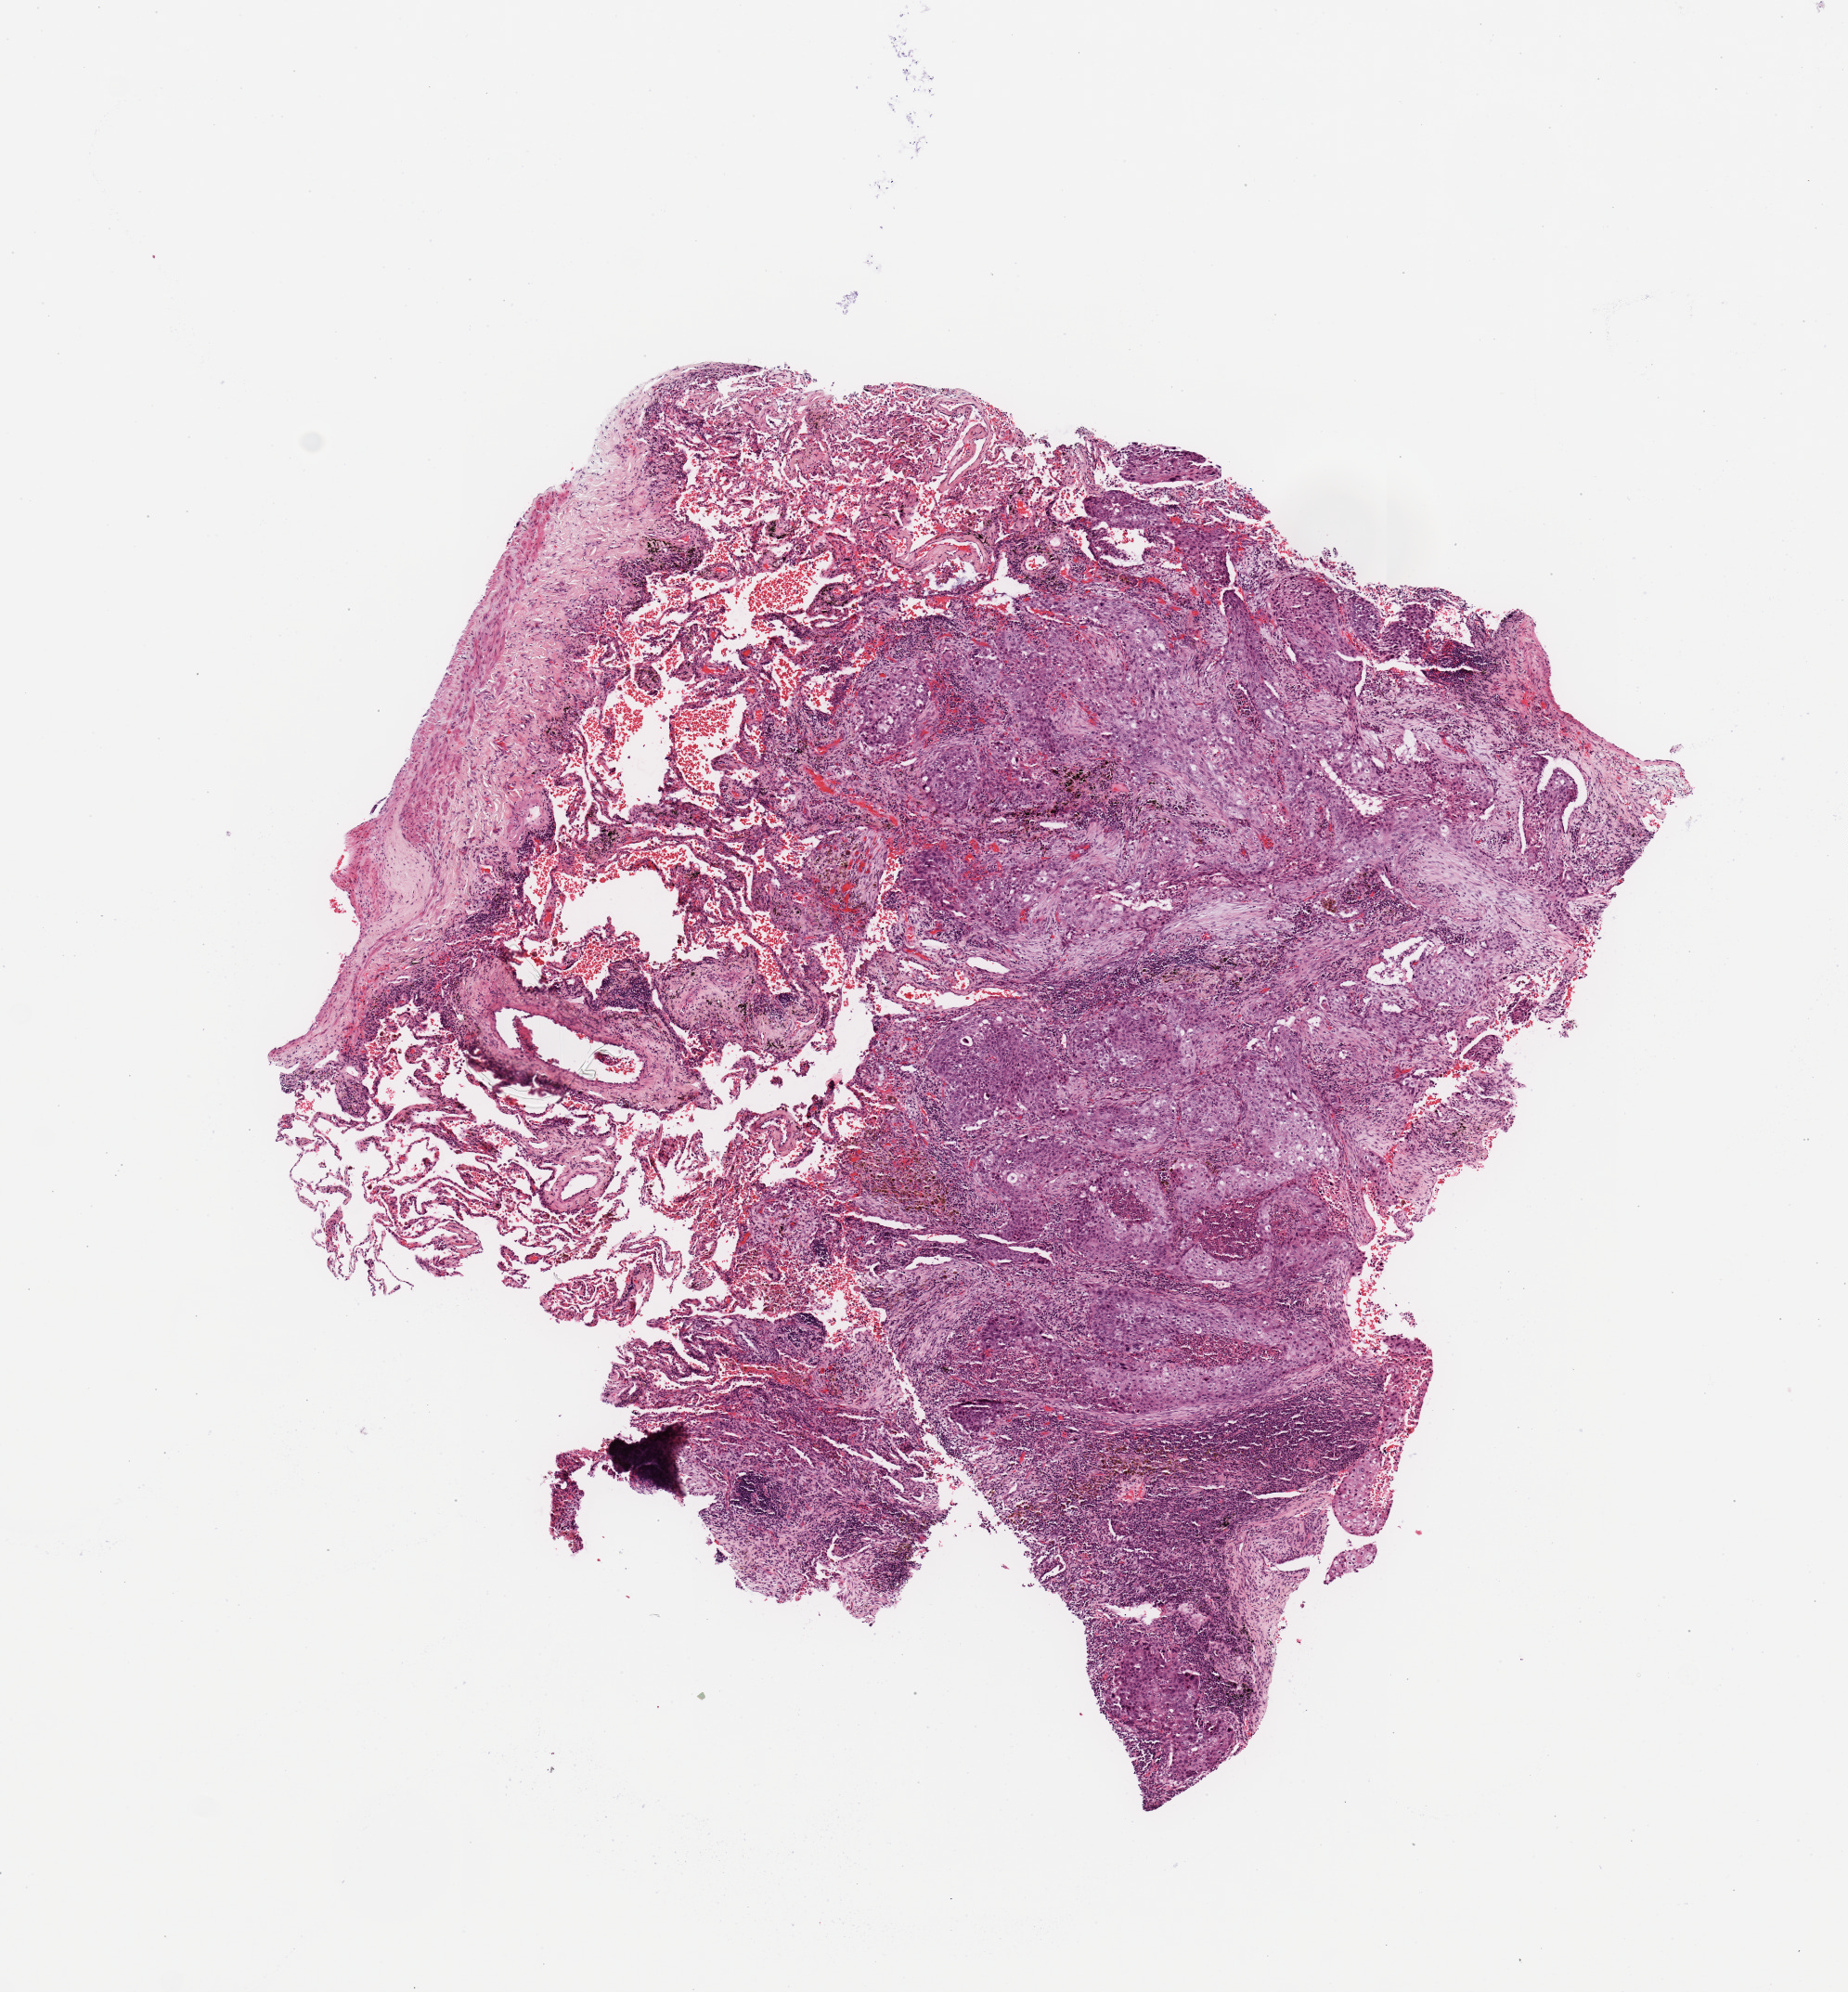
Whole-slide histology image, H&E-stained — a low-resolution overview of the entire scanned area, about 7.9 x 8.5 mm (from a 20x scan). Lung, tumour tissue. Male, 71 y/o. Histologic grade: G2 (moderately differentiated).
- AJCC pathologic stage: I
- diagnosis: Squamous cell carcinoma, NOS
- primary tumour site (as recorded): left lower lobe